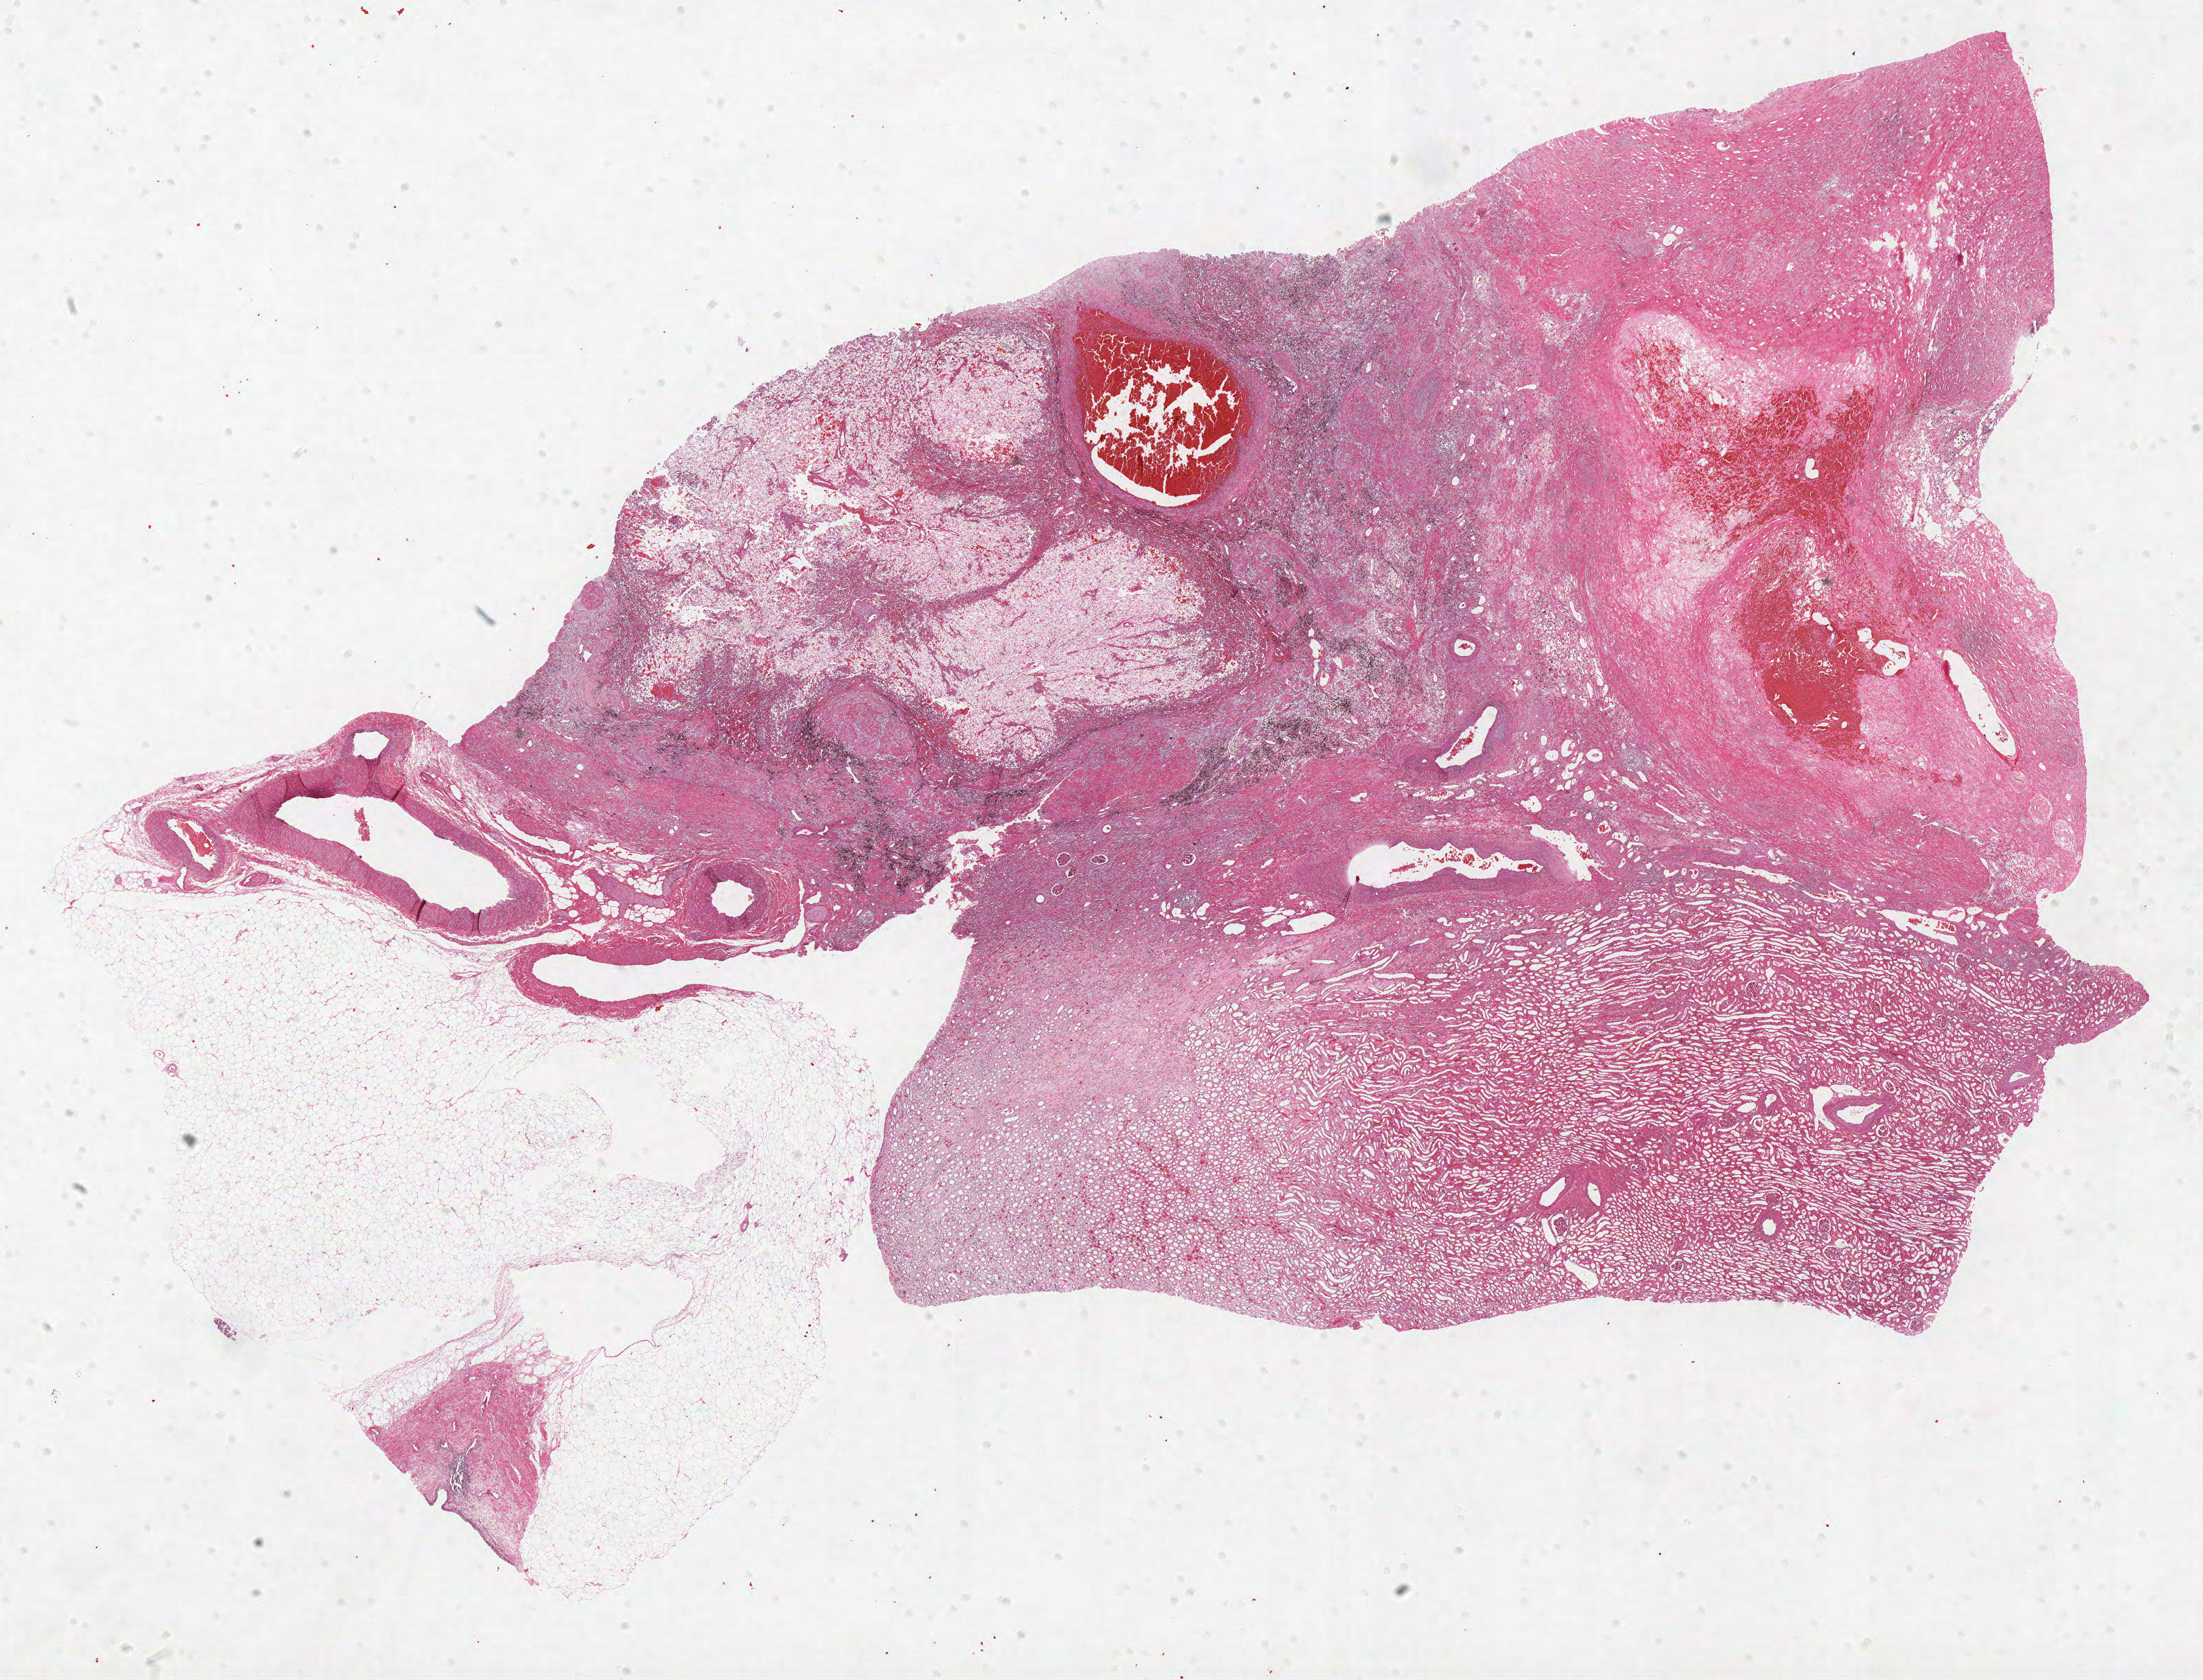
Whole-slide histology image, Hematoxylin and eosin (H&E) stained — low-resolution overview of the scanned area, about 25.4 x 19.4 mm, formalin-fixed paraffin-embedded (FFPE) diagnostic section, kidney, primary tumour sample. Male, age 59 years at initial diagnosis. Histologic grade: G2 (moderately differentiated).
Laterality: right. Pathologic diagnosis: Clear cell adenocarcinoma, NOS. AJCC pathologic stage: III.